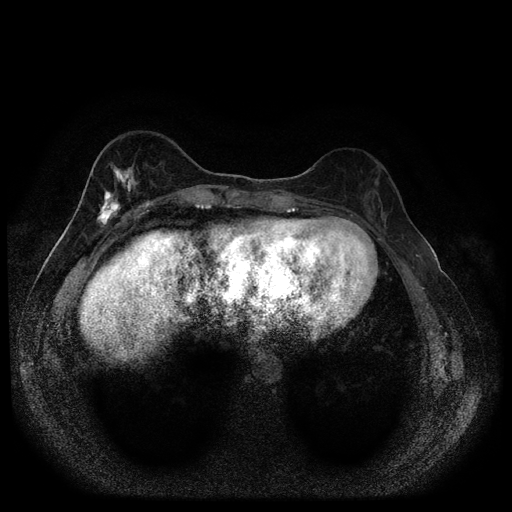
Breast MRI (dynamic contrast-enhanced, multi-phase), one axial slice; position 34 of 116 along the scan axis; dynamic contrast-enhanced series, time point 2 of 5 at this slice position (early post-contrast); 1.5 T; TE 2.7 ms, TR 5.4 ms; 512 × 512 image matrix, field of view 330 × 330 mm. Female patient, age 49 years.
Outlined on this slice (semi-automatically segmented with operator editing):
- breast lesion (labelled 'tumour' in the annotation; benign lesions carry a separate 'benign' label): bounding box <95,160,142,229> (left, top, right, bottom; pixels)